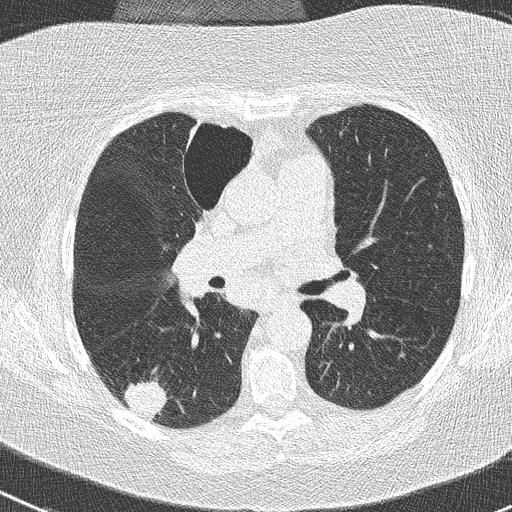
Low-dose screening chest CT, axial slice. Baseline screening round. Lung window (W 1500 / L -600 HU). 2 mm slice thickness. Lung (sharp) reconstruction kernel (B50f). Female participant, aged 74 years at enrolment. Former smoker at enrolment.
Expert-annotated lung lesion, box from (x=118, y=376) to (x=174, y=427) px. The screening reader recorded 3 non-calcified nodules or masses ≥4 mm on this exam; which of them this box marks is not recorded. Official screen result: positive, change unspecified: nodule(s) >= 4 mm or enlarging nodule(s), mass(es), or other non-specific abnormalities suspicious for lung cancer. Participant outcome: lung cancer diagnosed 16 days after this screen — non-small cell carcinoma, right lower lobe, poorly differentiated (G3), stage IIIA (AJCC 6th edition), 28 mm at pathology.